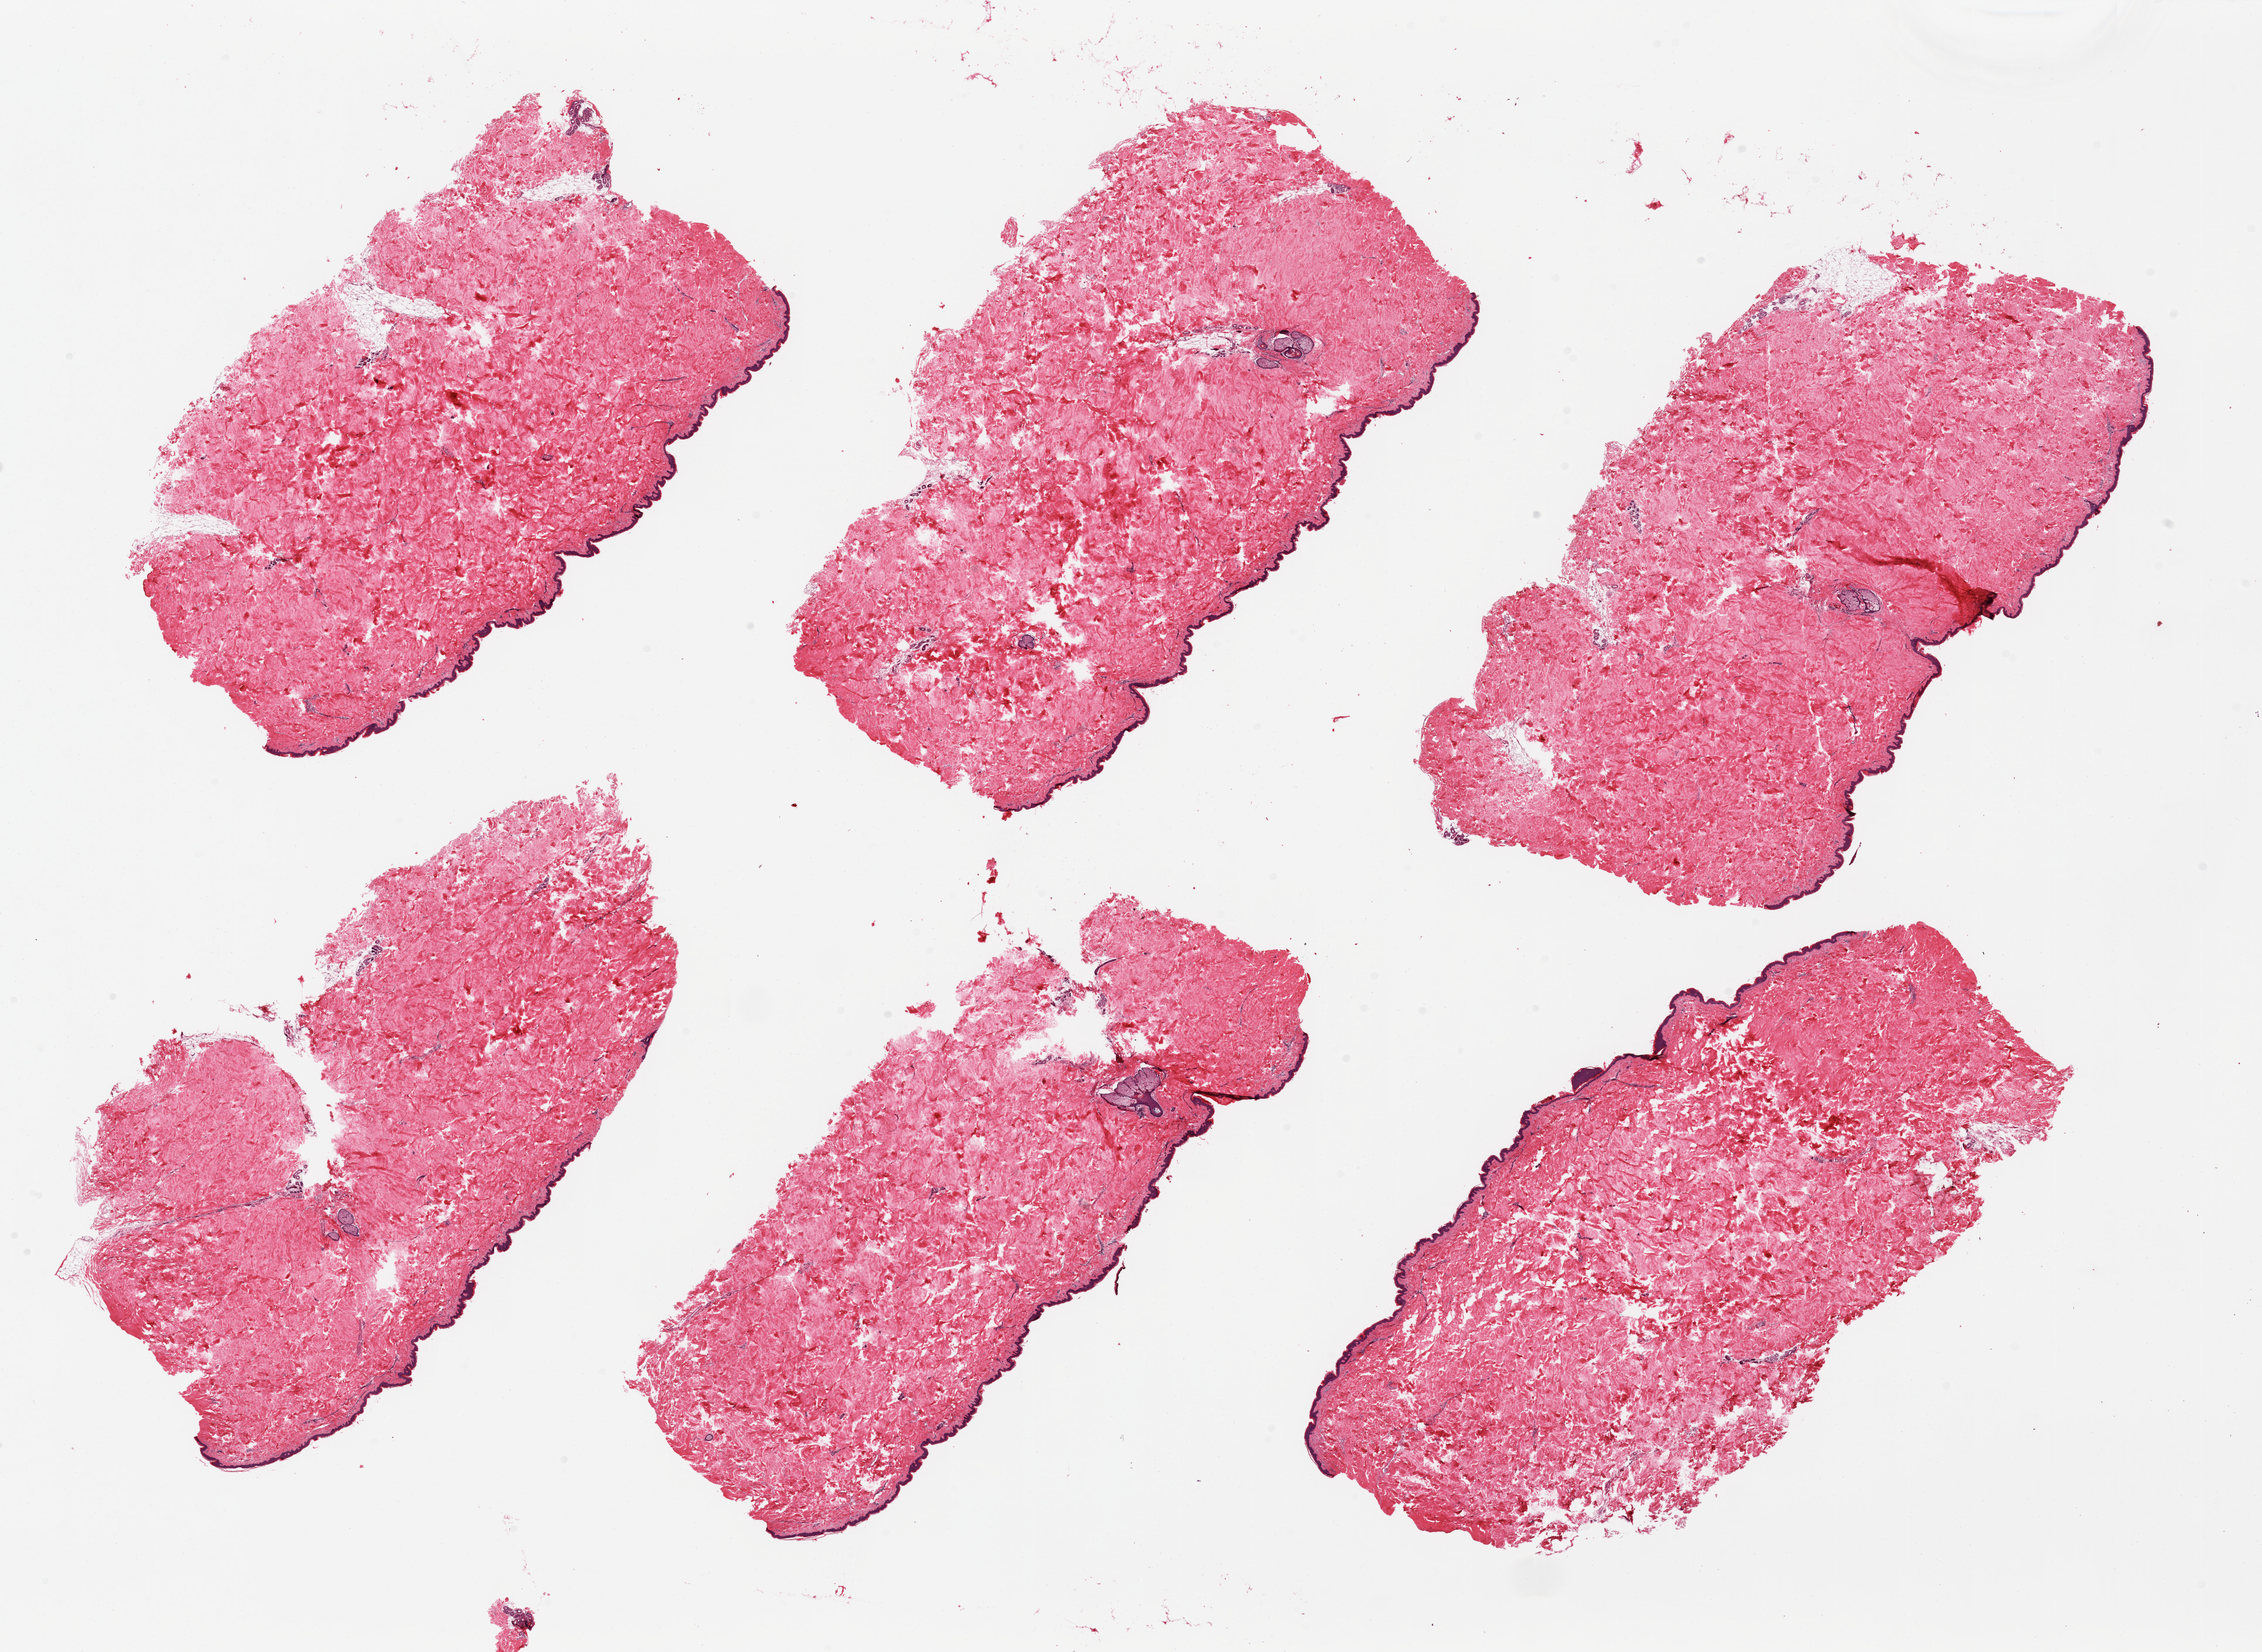
Whole-slide image, H&E stain — low-resolution overview of the scanned area, about 30.5 x 22.3 mm (acquisition: 20x scan), PAXgene-fixed paraffin-embedded (PFPE) section, target tissue: skin of suprapubic region, tissue donor sample. Female donor.
Reviewer comment on this tissue sample: 6 pieces, no dermal fat. Squamous epithelium is ~40 microns.